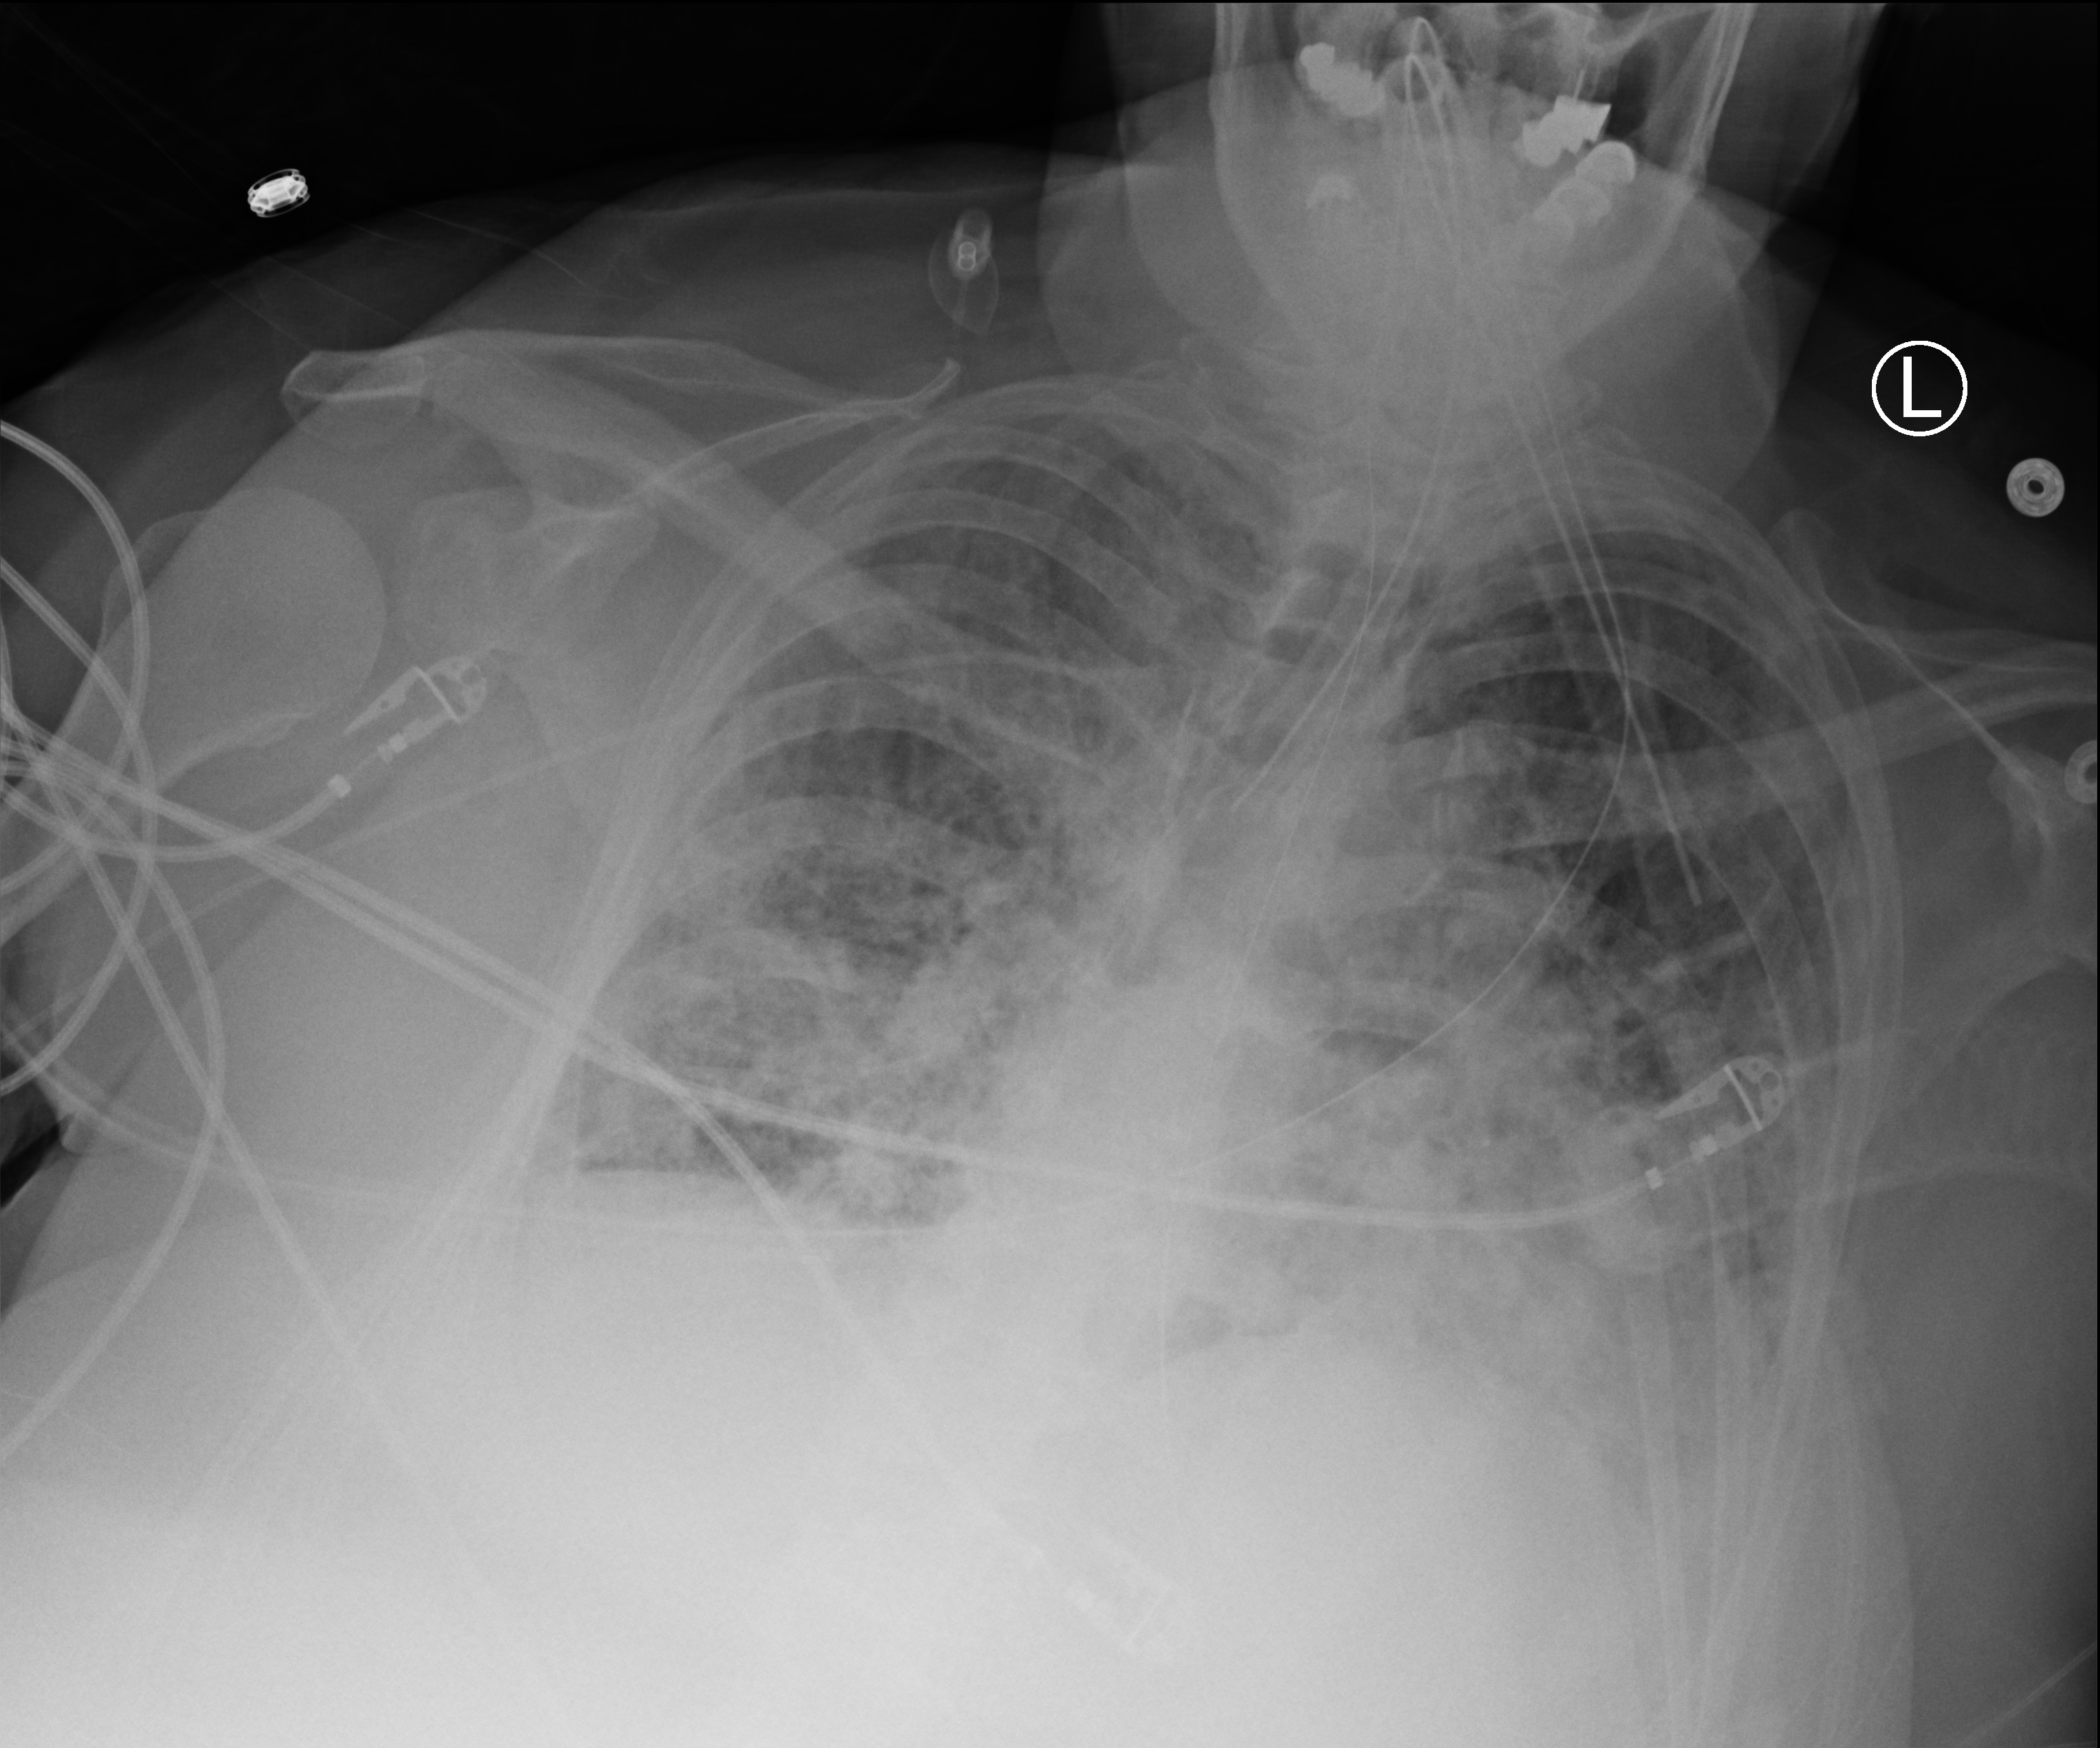
Chest X-ray (portable), anteroposterior (AP) projection. Patient hospitalised with COVID-19; female, aged 60–74 years.
From the hospital-stay record, not from the radiograph (when in the stay this image was taken is not recorded):
- mechanically ventilated during this hospital stay: yes